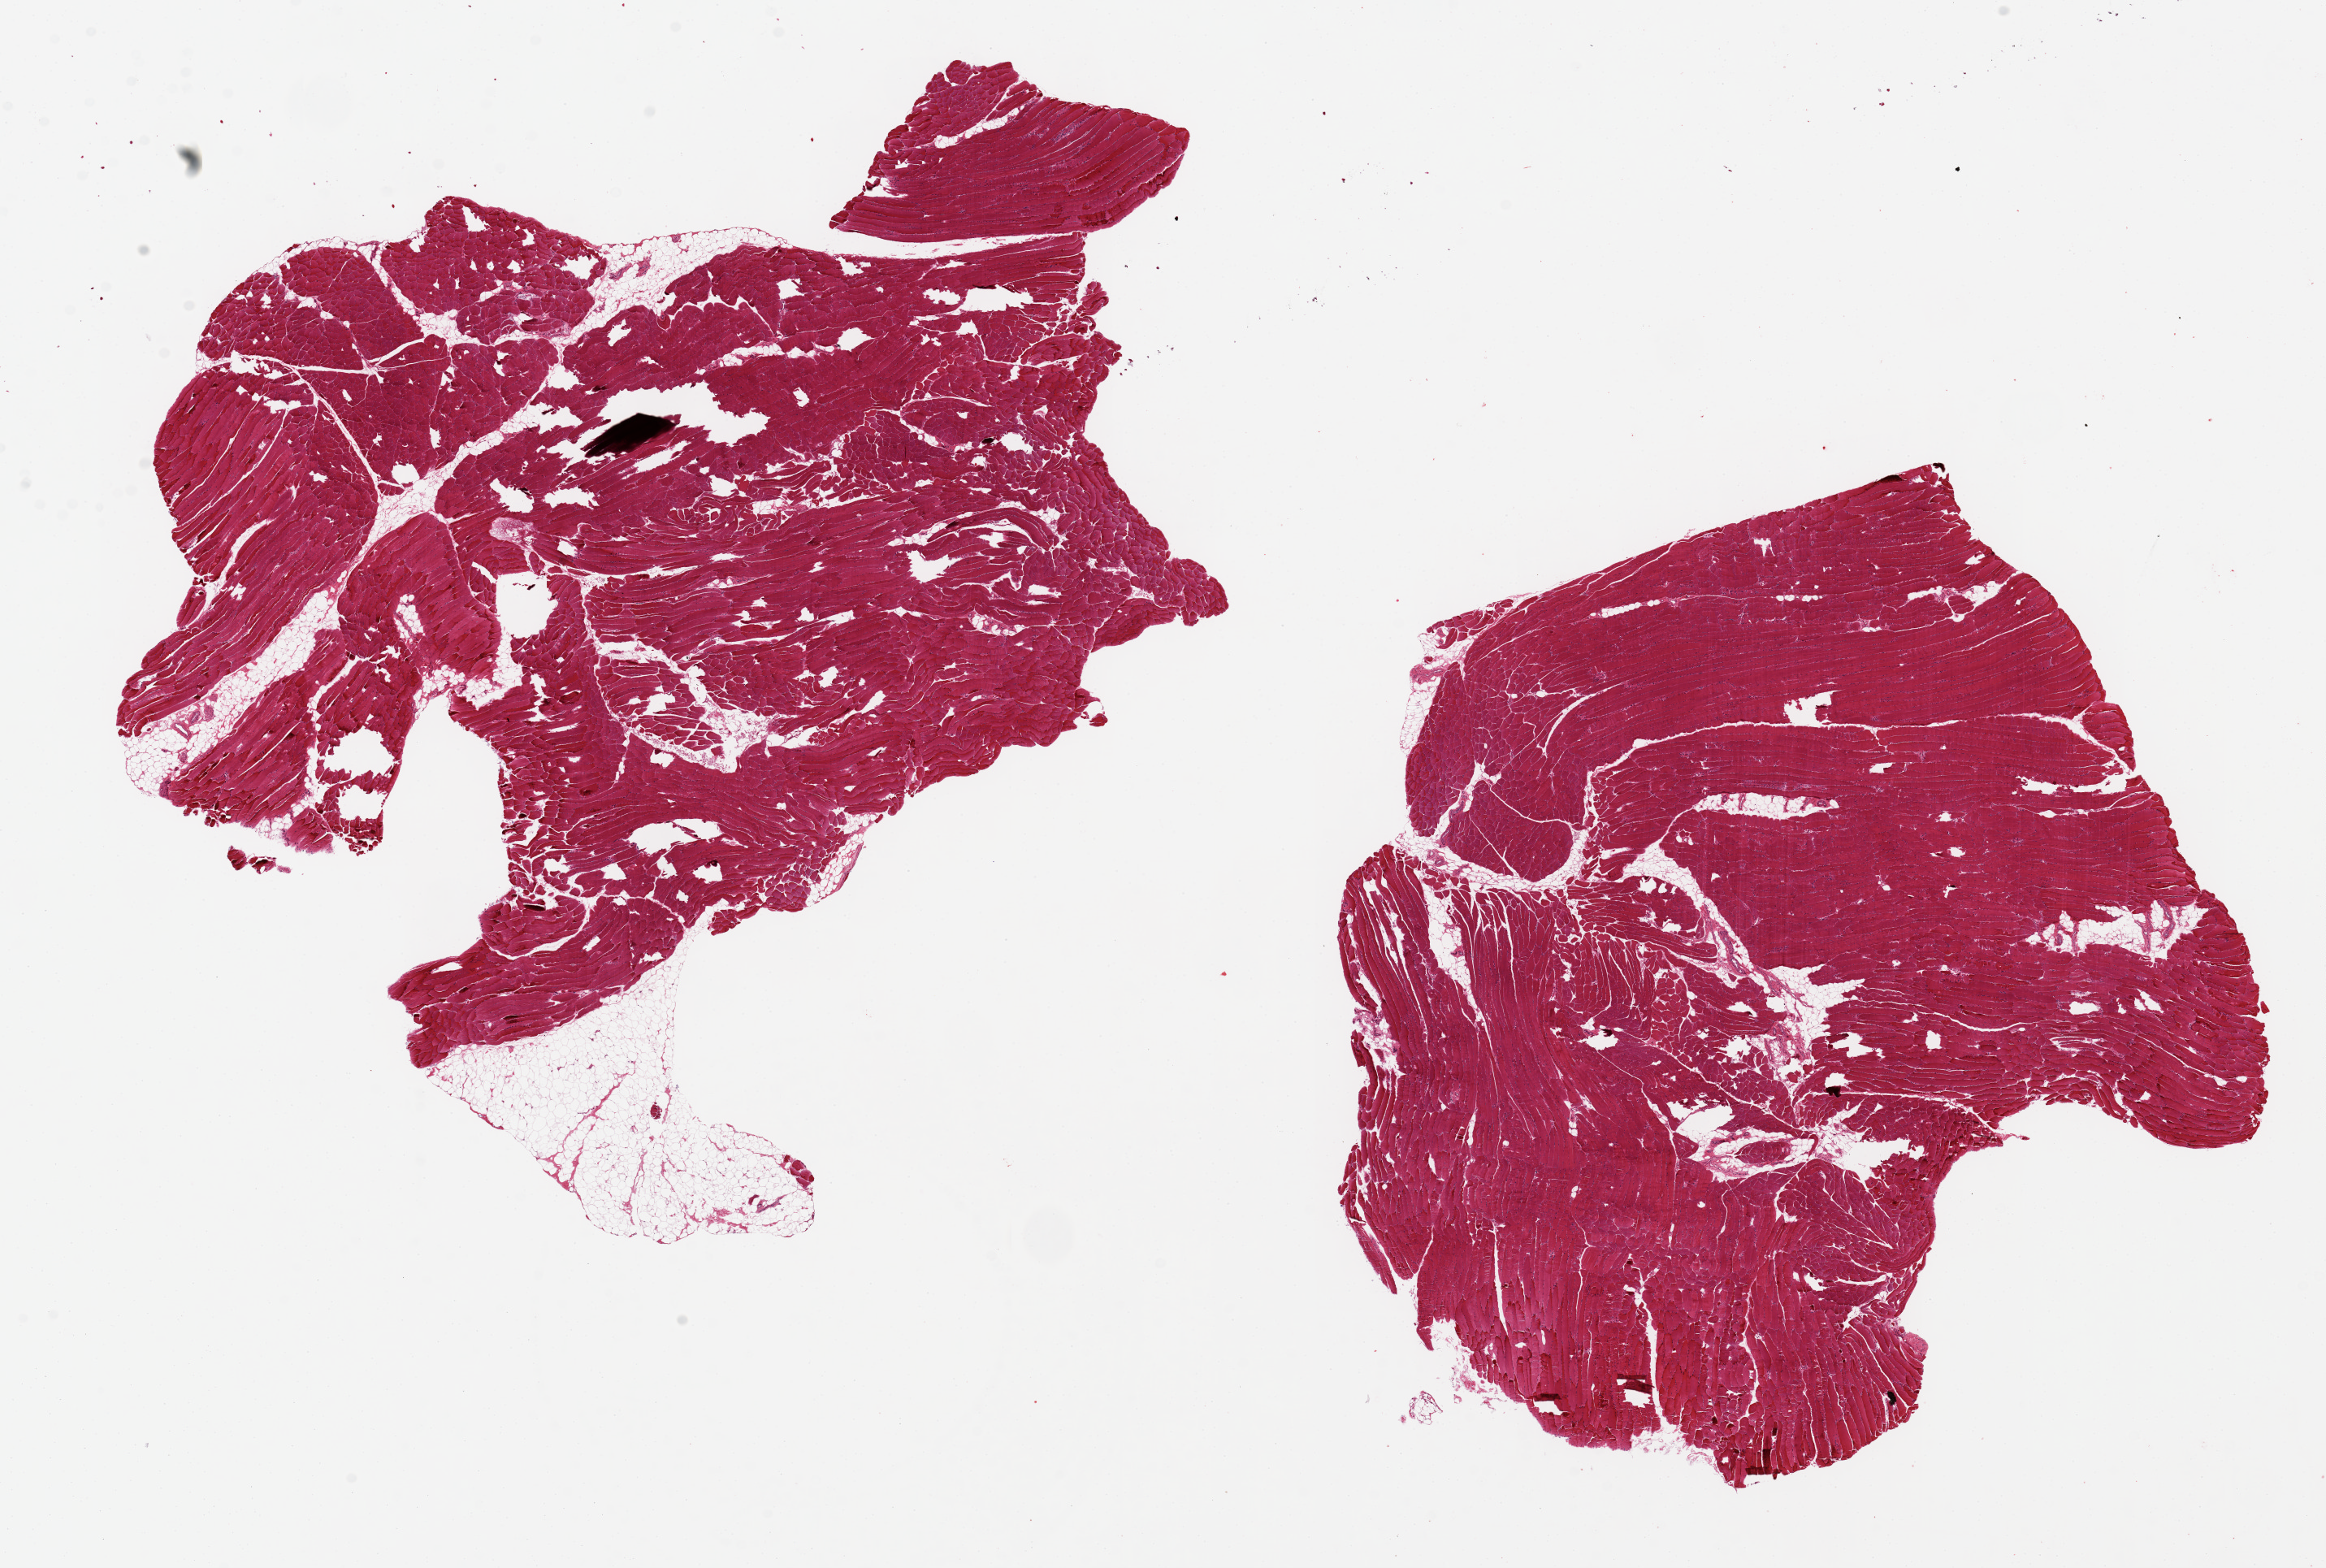
H&E whole-slide image — whole scanned area (about 22.6 x 15.3 mm, slide scanned at 20x) shown as a low-resolution overview, PAXgene-fixed paraffin-embedded (PFPE) section, target tissue: skeletal muscle, tissue donor sample. Donor sex: male.
Pathologist's review note for this sample: 2 pieces 12x8&9x9 mm; 10% adipose in 1; severe tissue tears.